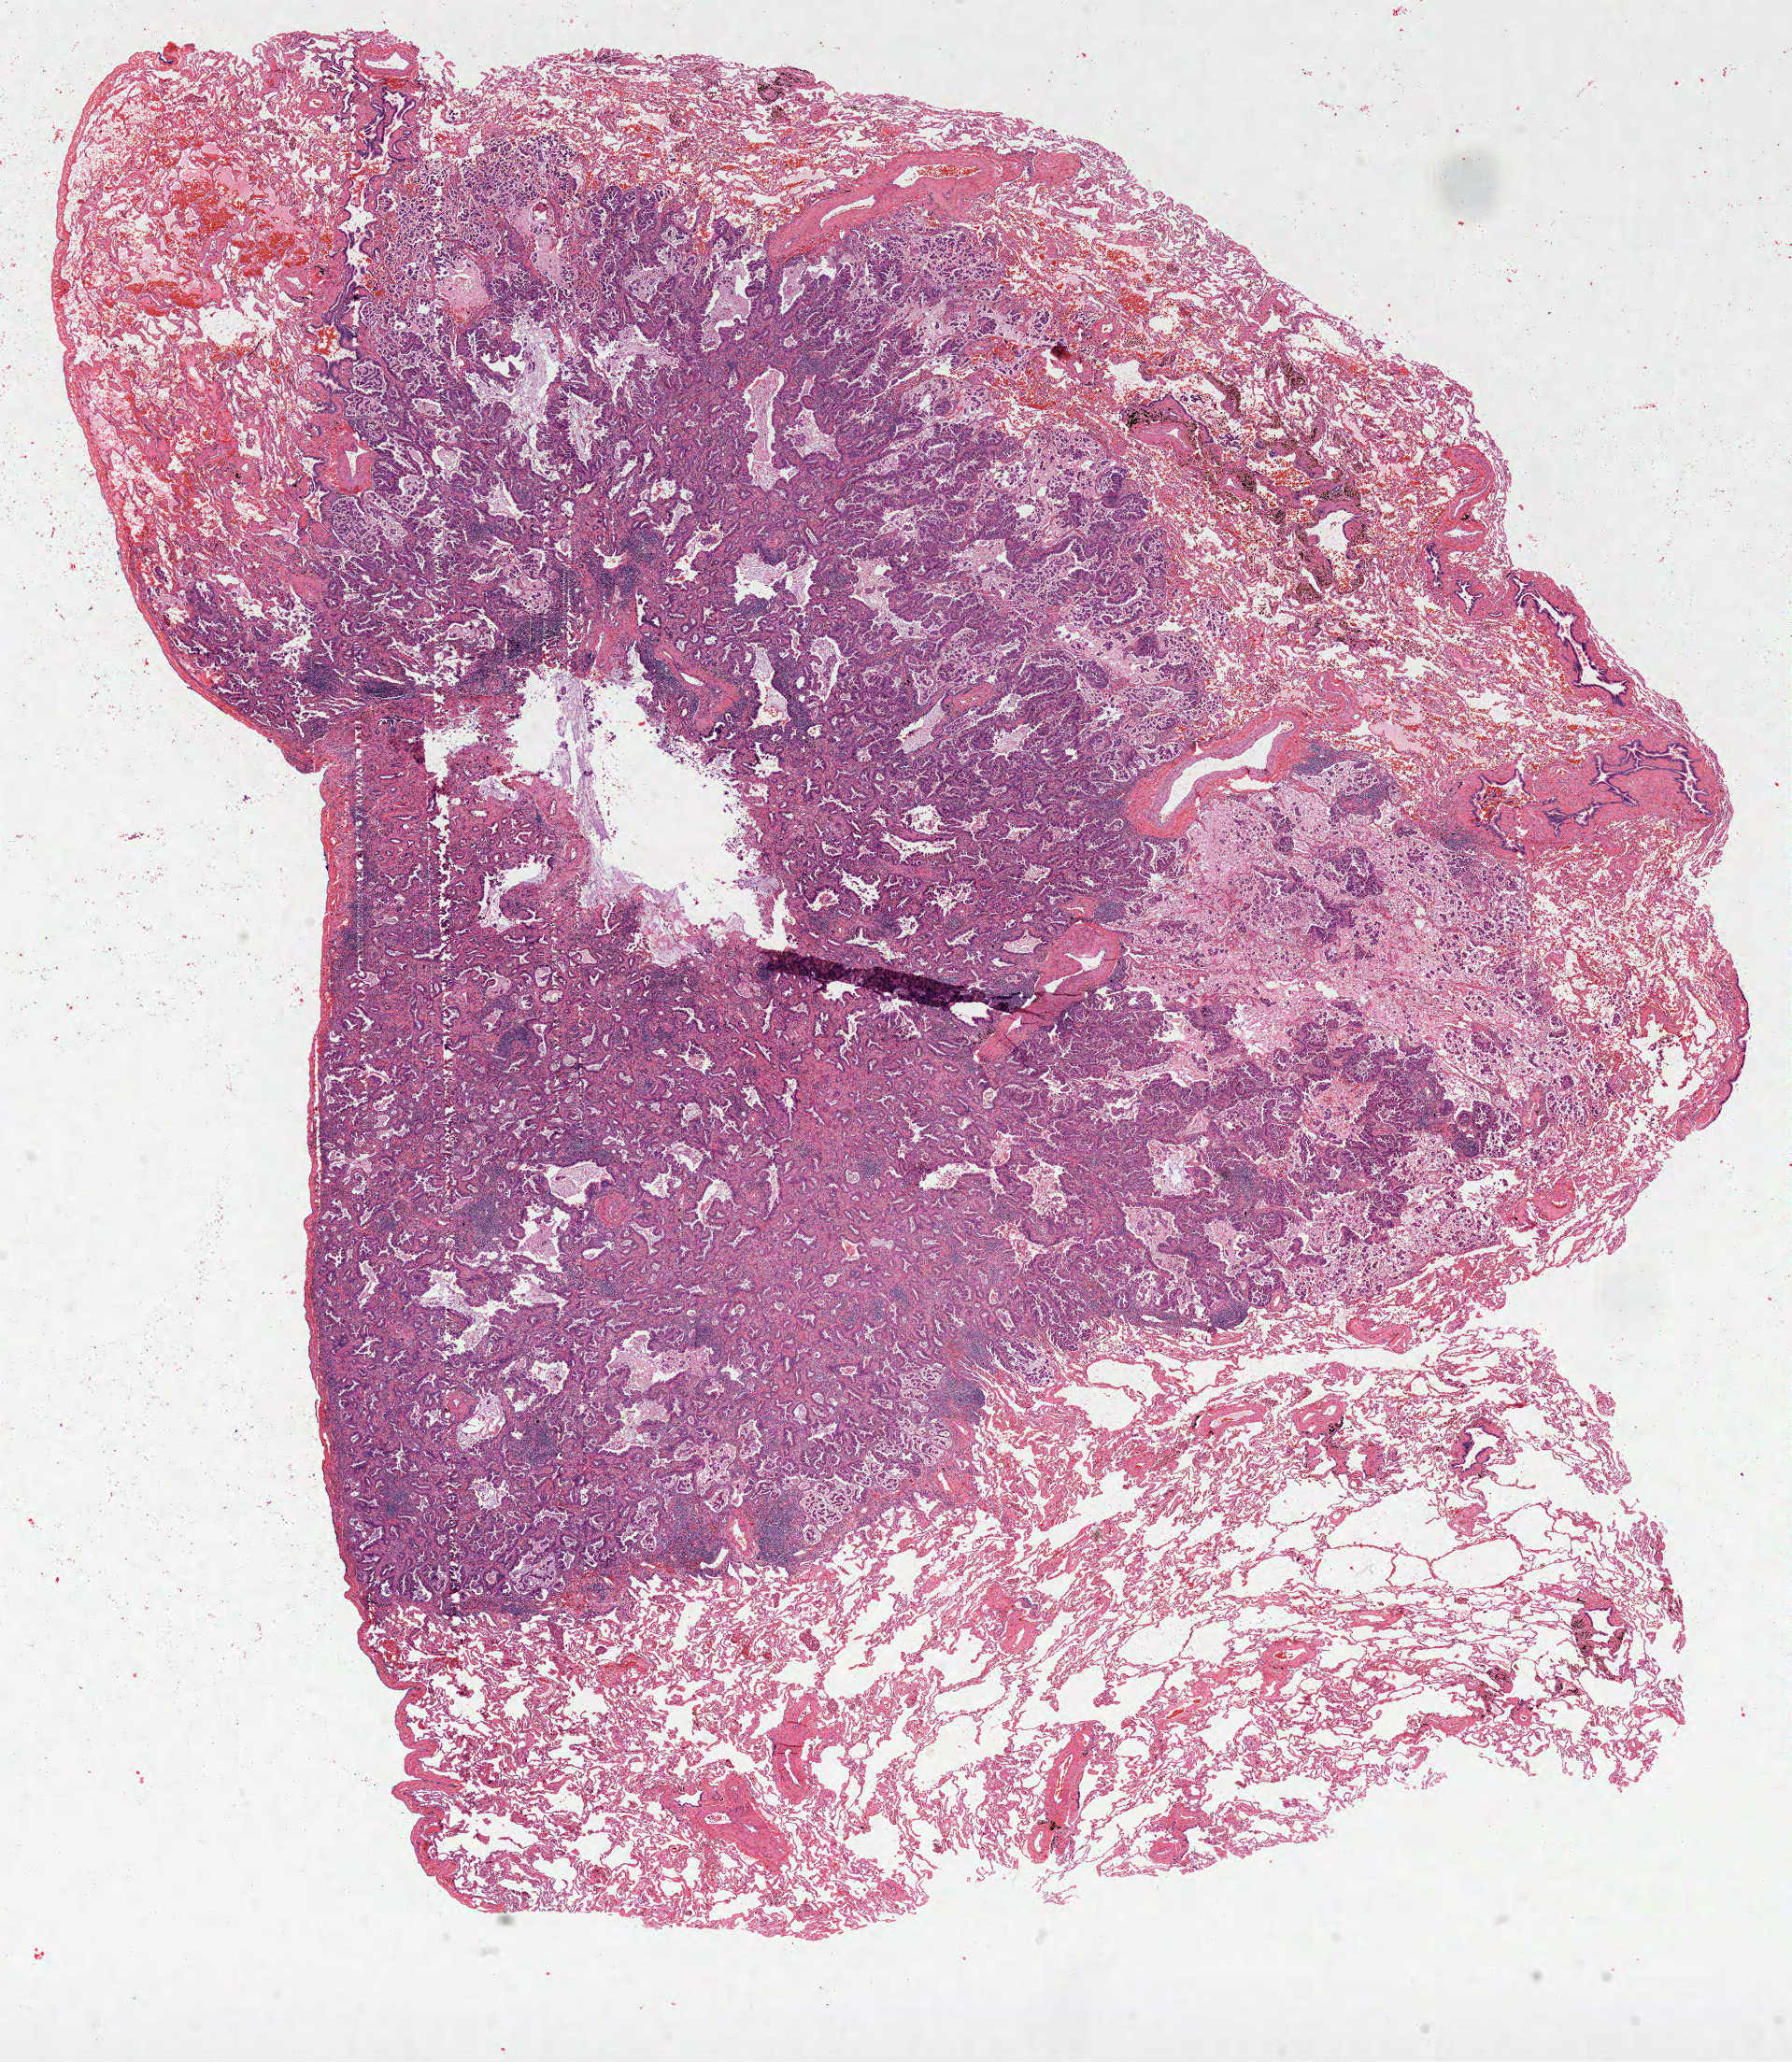
H&E whole-slide image — a low-resolution overview of the entire scanned area, about 15.5 x 17.8 mm (slide scanned at 40x), FFPE section, lung, primary tumour sample. Female patient; age at initial diagnosis 59 years.
Histologic diagnosis: Adenocarcinoma with mixed subtypes (lower lobe, lung). AJCC pathologic stage: IIA (7th edition).